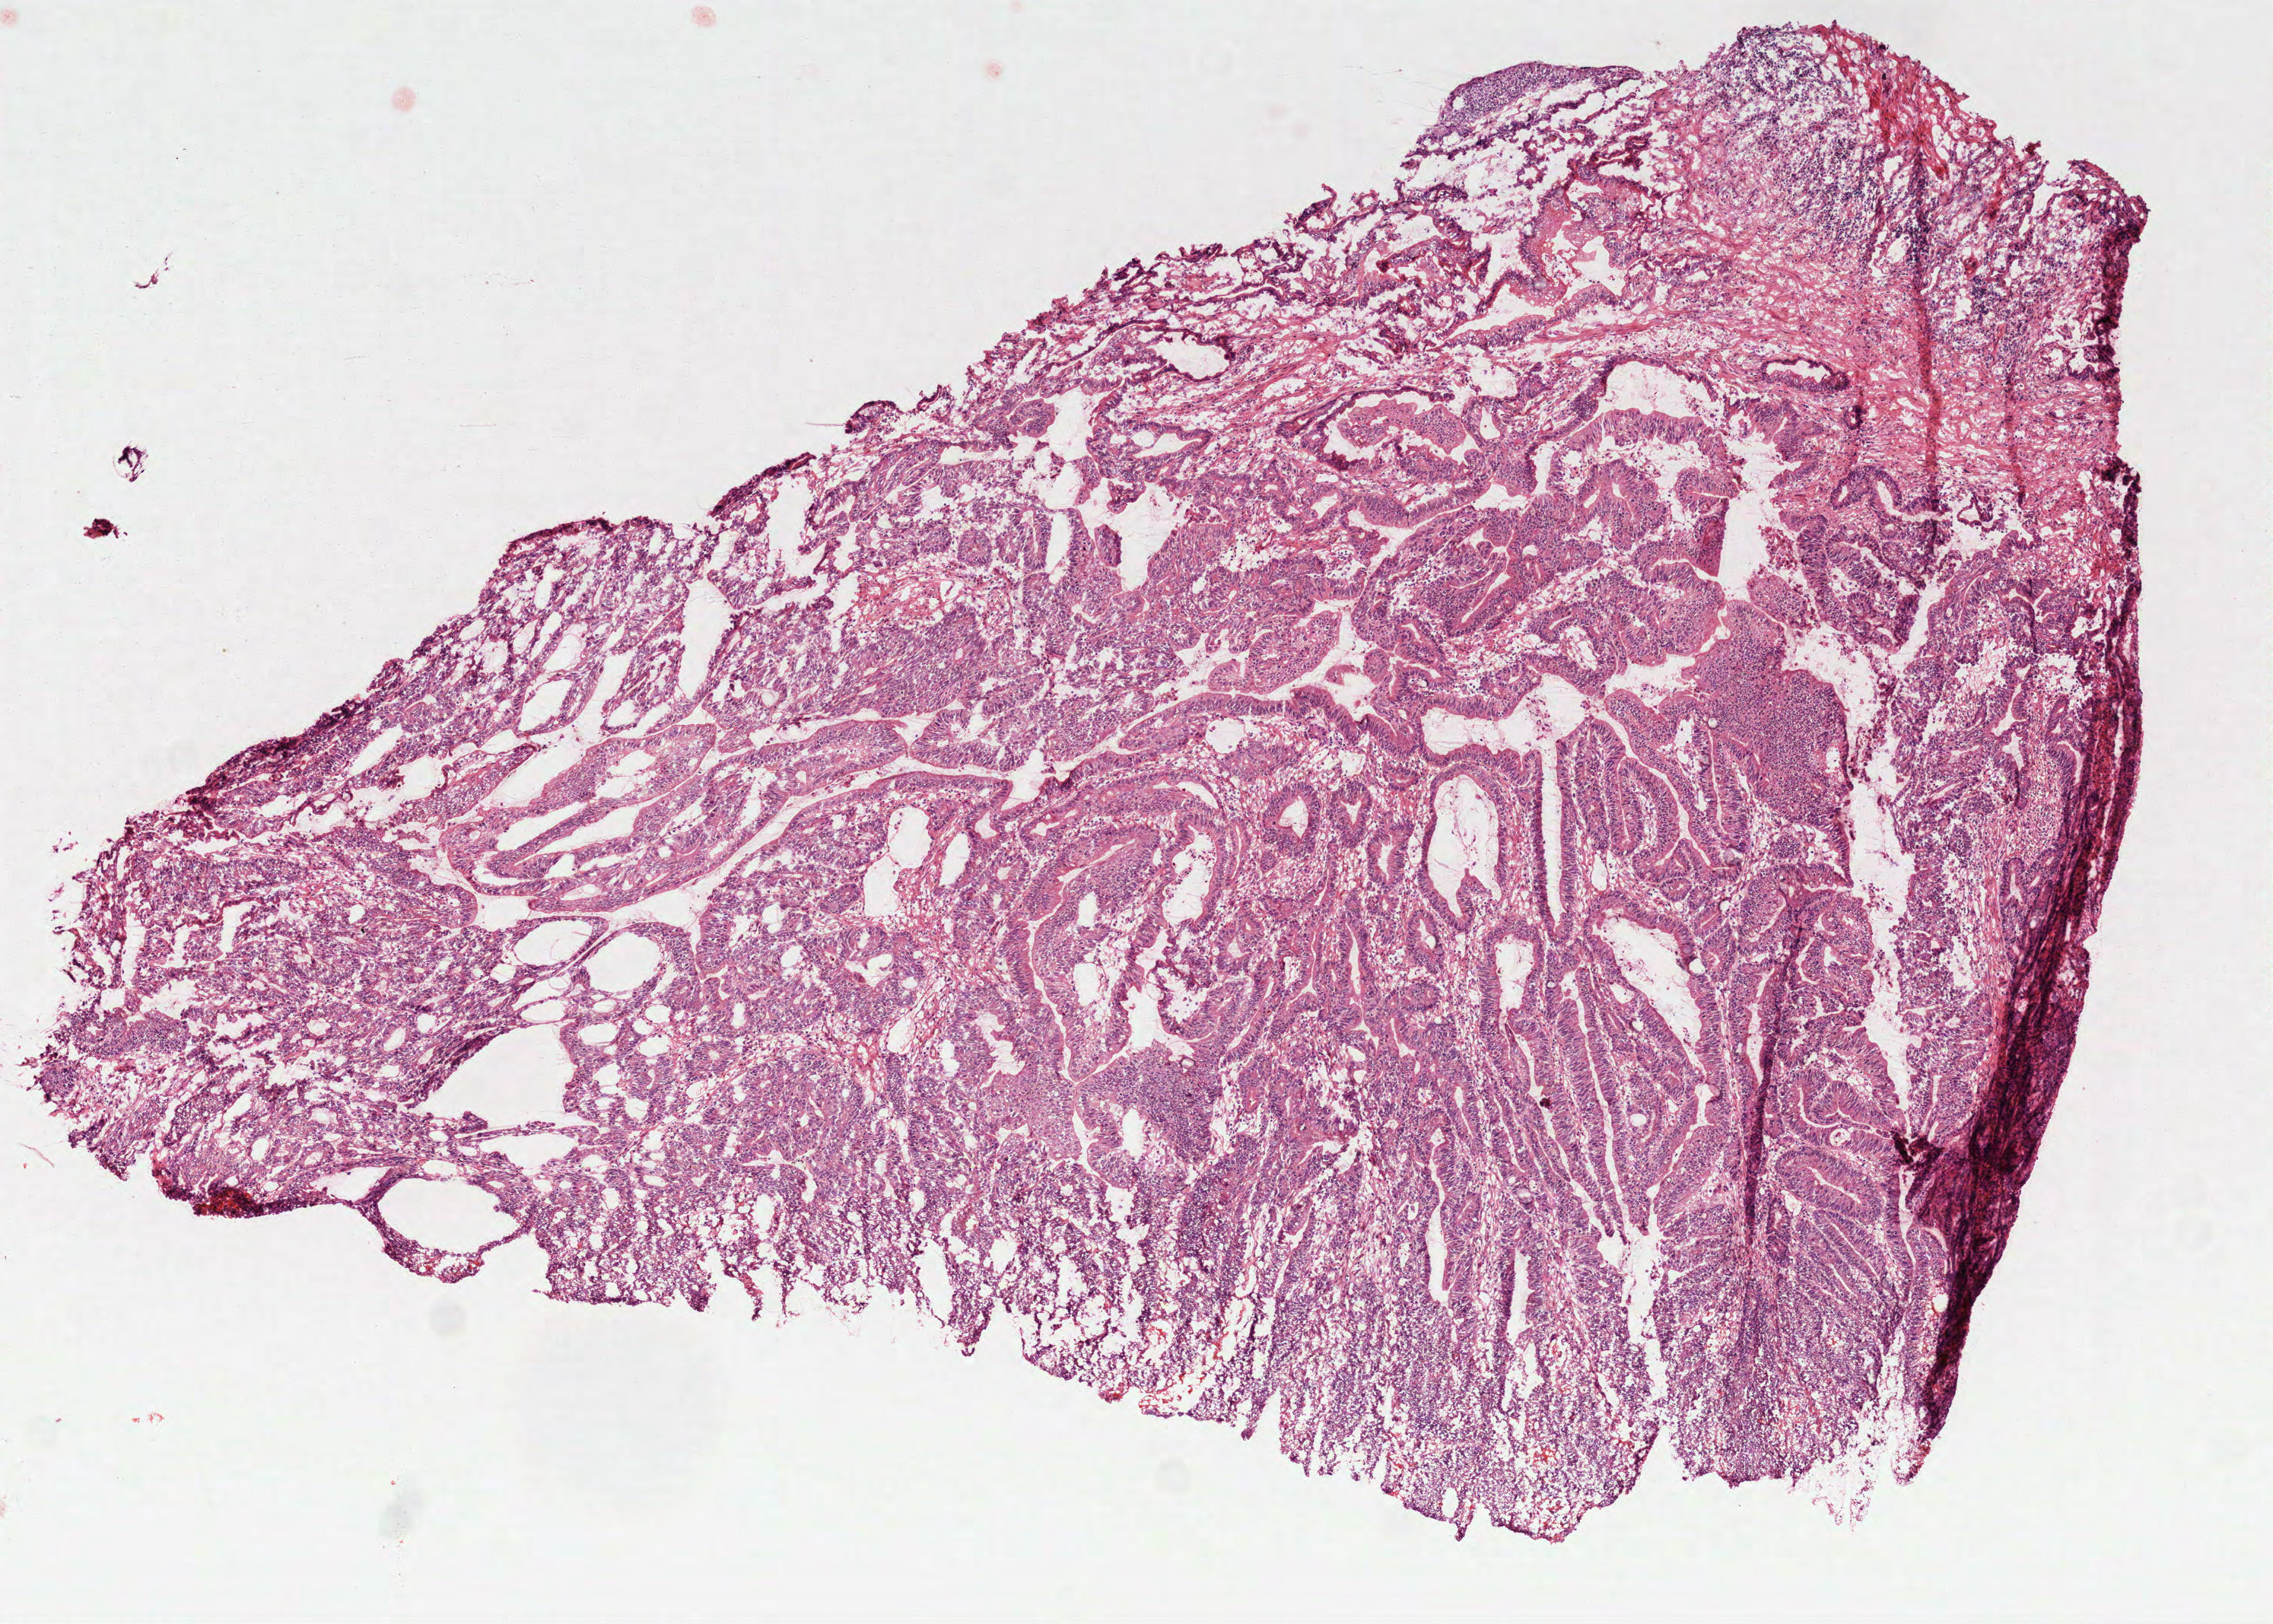
Digitized H&E tissue section (whole slide) — whole scanned area (about 6.0 x 4.3 mm, from a 40x scan) shown as a low-resolution overview. Frozen section from the top of the tissue portion. Sample: primary tumour, colon. Patient: female, age at initial diagnosis 79 years.
Histologic diagnosis: Mucinous adenocarcinoma (cecum).